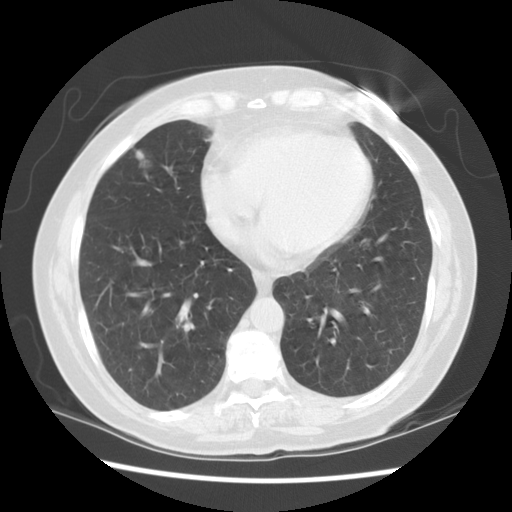
Low-dose screening chest CT, axial slice, second annual screen, lung window (W 1500 / L -600 HU), slice 45 of 115 in the series, 512 × 512 image matrix, field of view 340 × 340 mm. Female participant, aged 71 years at enrolment.
• Expert-annotated lung lesion, bounding box (x1, y1, x2, y2) in pixels: (112, 131, 167, 191).
• The exam's reader record, not a measurement of the box and not confirmed to be the same lesion: non-calcified nodule or mass ≥4 mm, right middle lobe, 6 × 6 mm, spiculated (stellate) margins, soft tissue attenuation, pre-existing on the prior screen: yes; interval growth: yes.
• Official screen result: positive, other.
• Later outcome: lung cancer diagnosed 68 days after this screen — adenocarcinoma, NOS, right middle lobe, moderately differentiated (G2), stage IA (AJCC 6th edition), 12 mm at pathology.